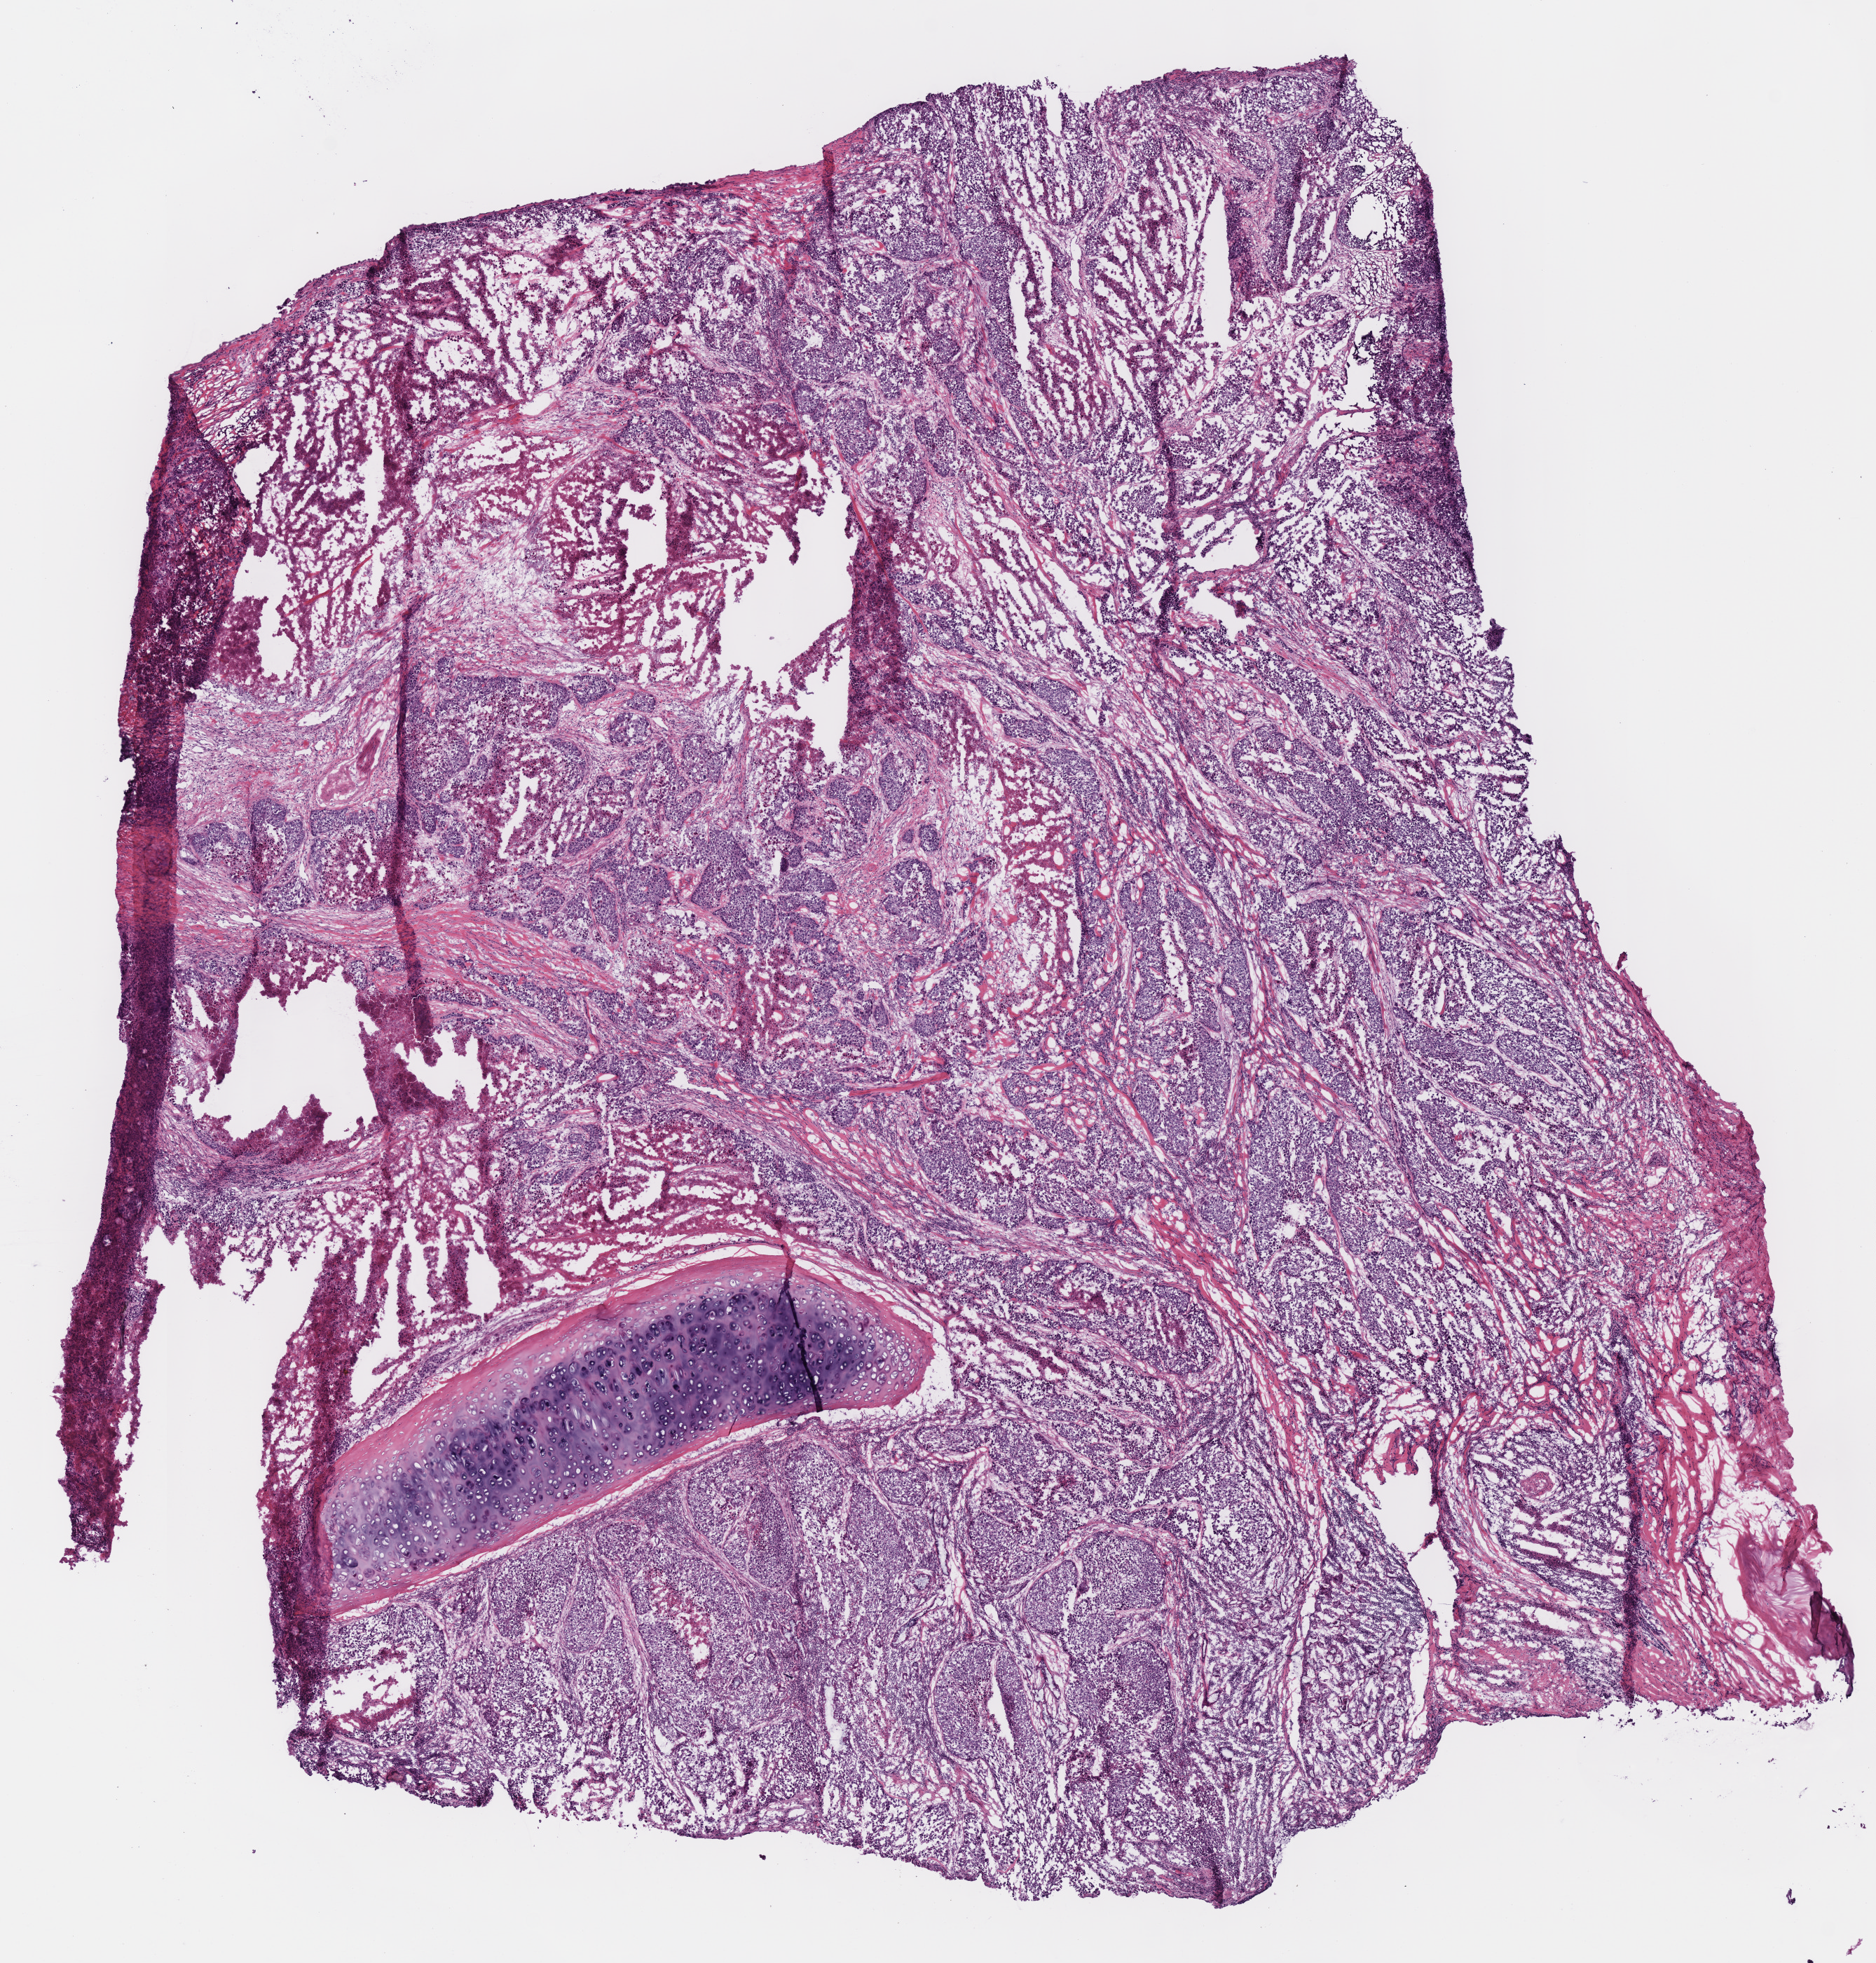
Whole-slide histology image, H&E-stained — low-resolution overview of the scanned area, about 10.5 x 11.0 mm. Frozen section from the top of the tissue portion. Sample: primary tumour, lung. Male patient; age at initial diagnosis 50 years. Composition of this section per pathologist review: tumour cells 92%, tumour nuclei 75%, normal cells 8%, stromal cells 0%, necrosis 0%. Inflammatory infiltration, as recorded: lymphocyte infiltration 20%, monocyte infiltration 0%, neutrophil infiltration 0%.
AJCC pathologic stage: IIA. TNM: T2a N1 M0. Histologic diagnosis: Squamous cell carcinoma, NOS (upper lobe, lung).